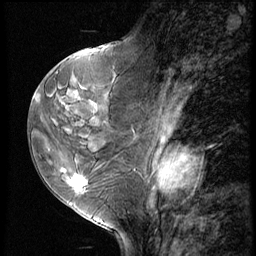
Breast MRI (dynamic contrast-enhanced), one sagittal slice; position 29 of 60 along the scan axis; 3 images stored at this slice position (order not interpretable as contrast timing); 1.5 T; TE 4.2 ms, TR 8.9 ms; 2.5 mm slice thickness; 256 × 256 image matrix, field of view 200 × 200 mm. Female patient, age 50 years. Case-level facts recorded for this patient, not image findings: setting: breast cancer imaged before/during neoadjuvant chemotherapy; receptor status: HR-positive, HER2-negative.
Annotated regions visible in this slice (semi-automatic segmentation, software-assisted and operator-edited):
- analysis volume of interest (the breast-tissue region the enhancement analysis was run in; not a lesion): bounding box [x1, y1, x2, y2] px = [38, 102, 118, 213]
- tumour enhancement mask (voxels above the 140 % enhancement threshold inside the analysis volume of interest): [63, 170, 88, 191]